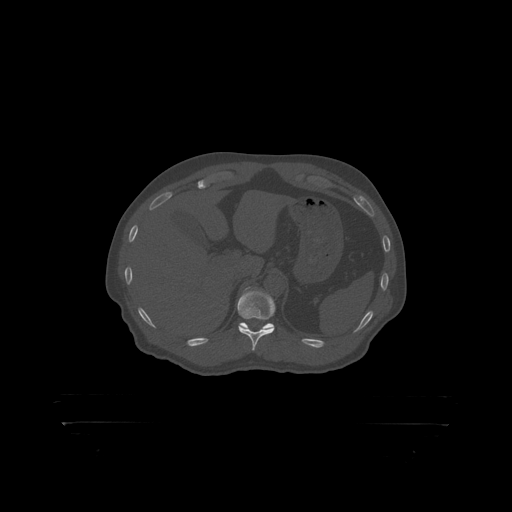
CT including the spine, one axial slice; slice 371 of 399 in the series (ordered by position); reconstruction kernel STANDARD; 120 kVp; bone window (W 1800 / L 400 HU); 512 × 512 image matrix, field of view 650 × 650 mm. Patient: male, 46 years. From the clinical record (not read from this slice): primary cancer: skin.
Structures marked on this image (semi-automatically segmented with operator editing):
- T11 vertebra: bounding box (x1, y1, x2, y2) in pixels: (238, 287, 276, 319)